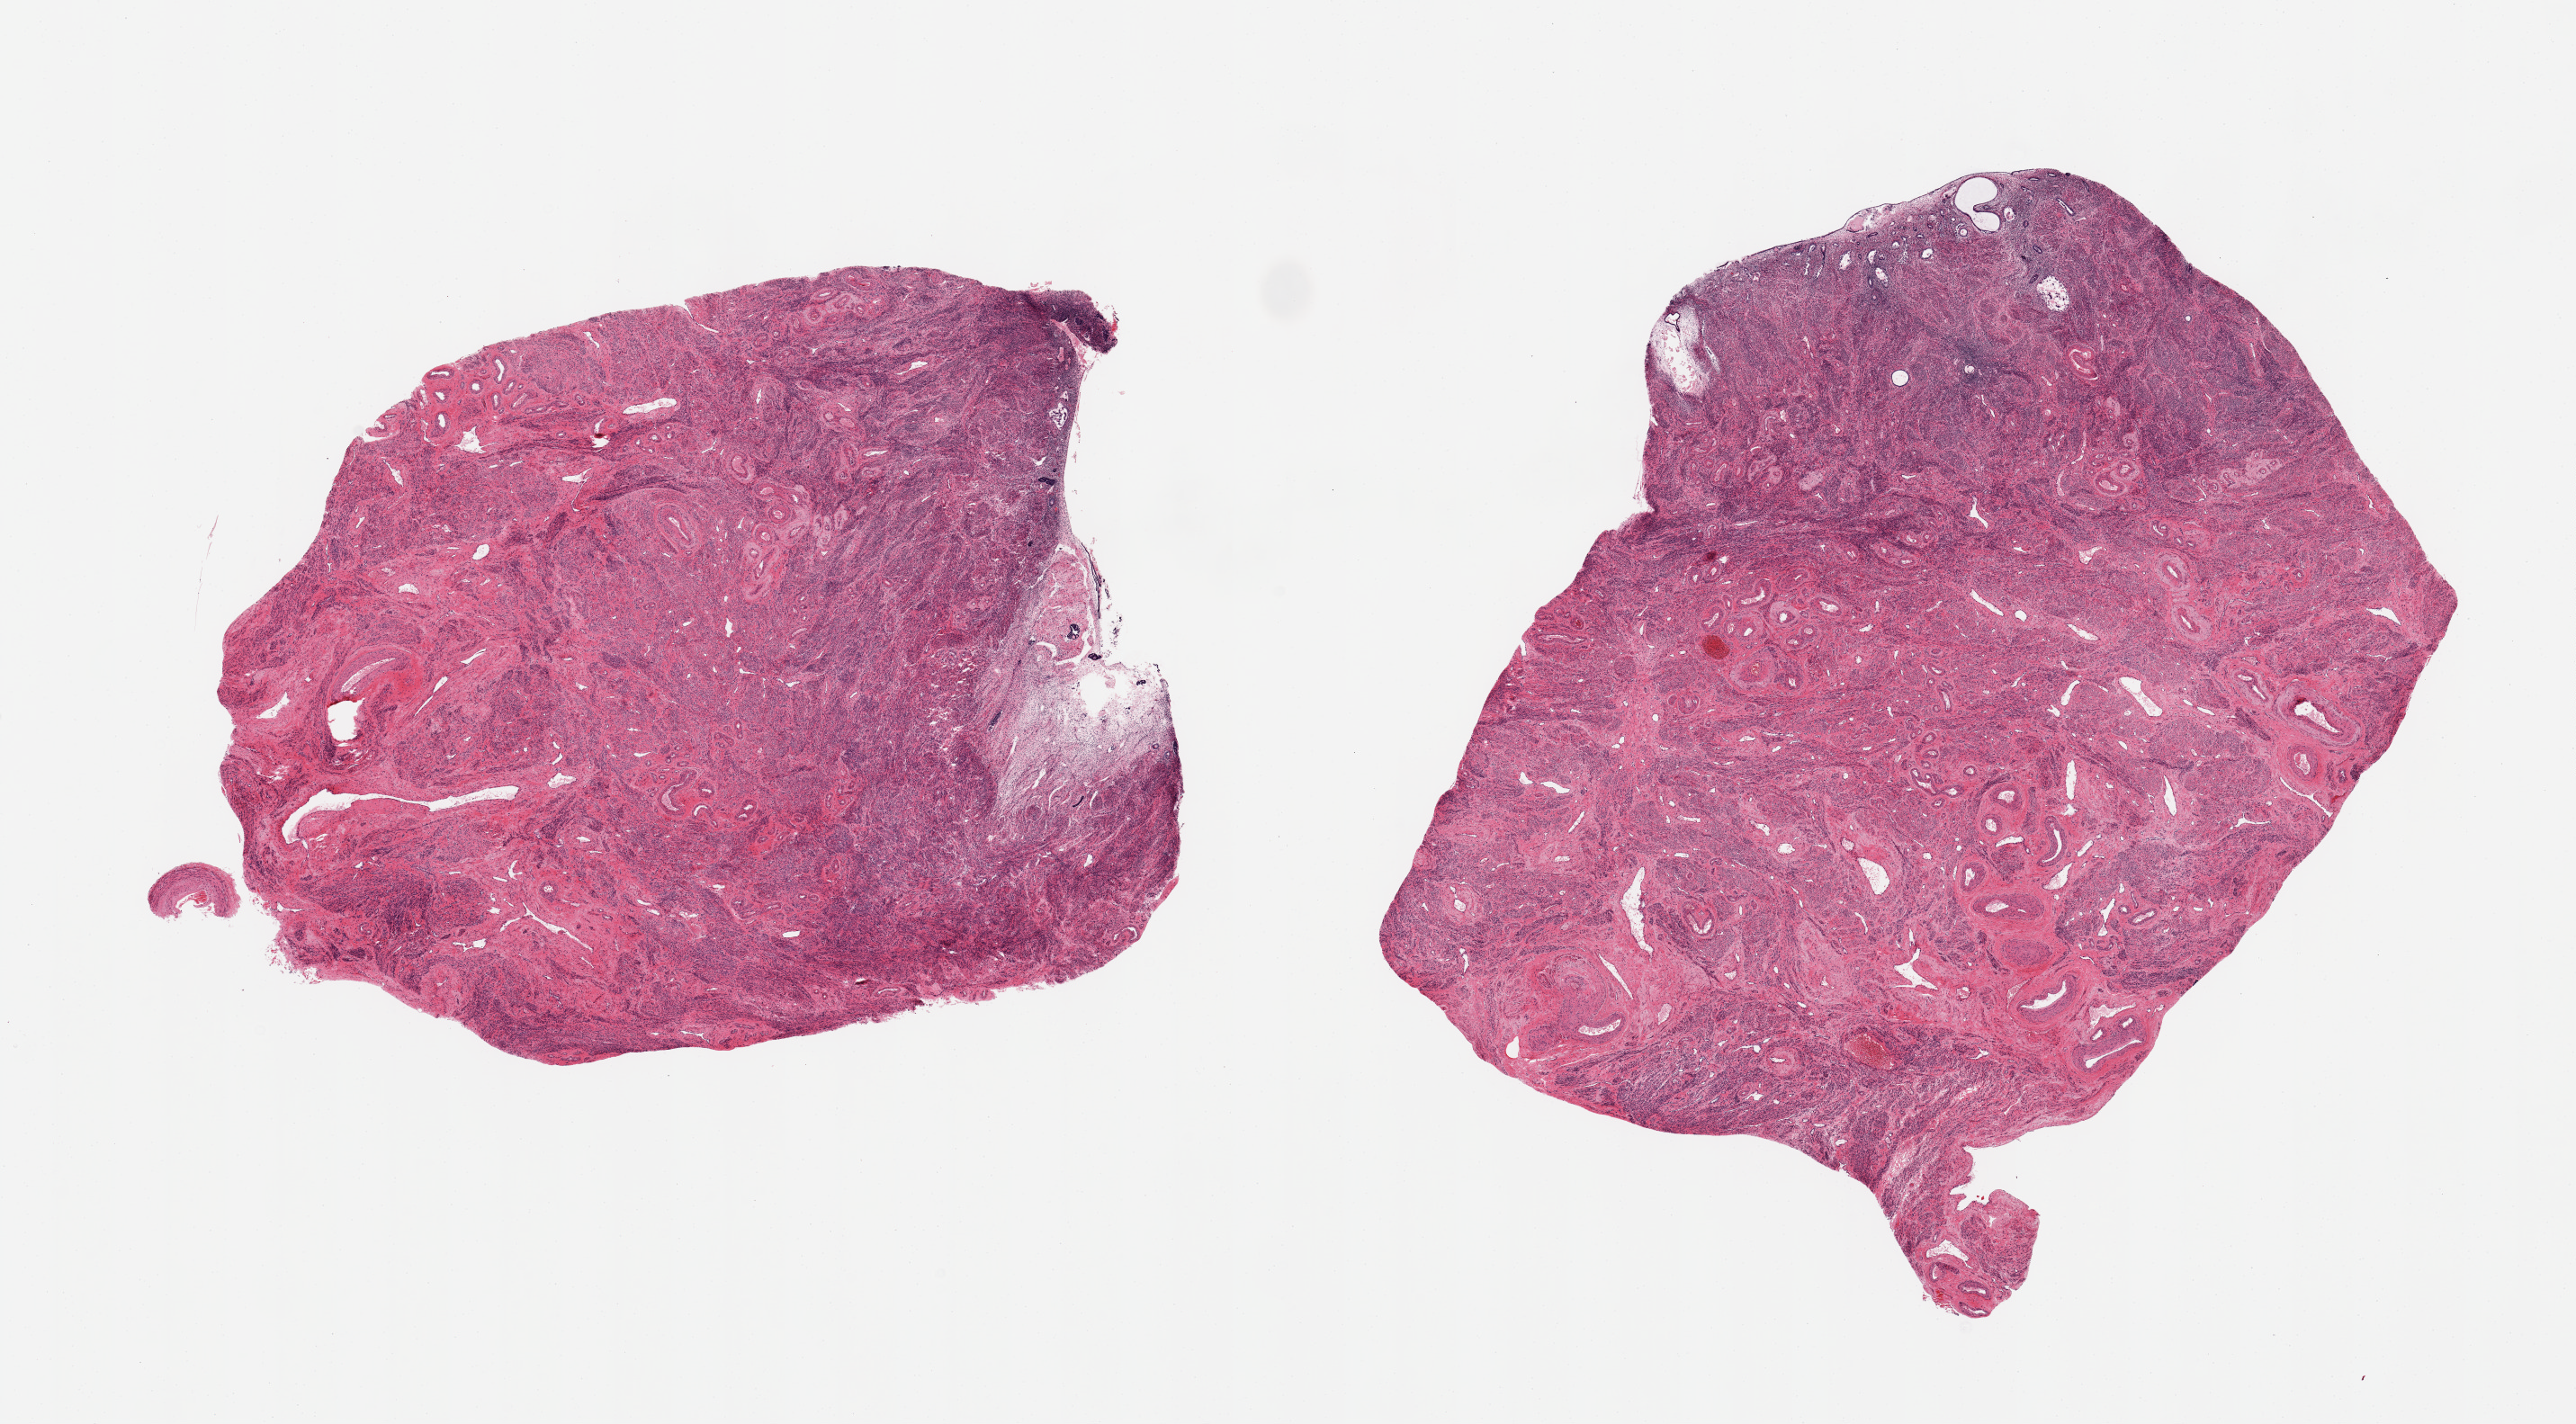
Digitized hematoxylin and eosin (H&E)-stained section — whole scanned area (about 22.6 x 12.5 mm) shown as a low-resolution overview. PAXgene-fixed paraffin-embedded (PFPE) section. Section of uterus (target tissue). Donor tissue sample. Donor sex: female.
Pathologist's review note for this sample: 2 pieces; atrophic endometrium and myometrium.